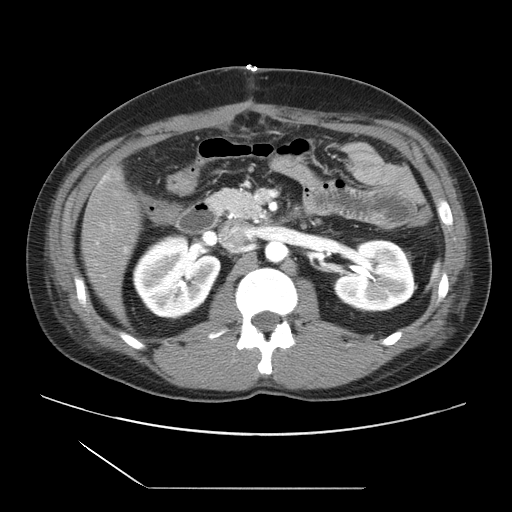
Contrast-enhanced abdominal CT, one axial slice. Slice 7 of 39 in the series (ordered by position). Intravenous contrast given. Soft-tissue window (W 400 / L 40 HU). 5 mm slice thickness. 512 × 512 image matrix, field of view 395 × 395 mm. Male patient, age 39 years. Case-level facts recorded for this patient, not image findings: diagnosis: colorectal cancer liver metastases, imaged before liver resection; multiple liver metastases: yes; largest metastasis: 1.3 cm; disease in both lobes: no.
Annotated regions visible in this slice (outlined manually by an expert reader):
- liver: bounding box [x1, y1, x2, y2] px = [82, 170, 141, 318]
- portal vein (with intrahepatic branches): [97, 242, 127, 252]